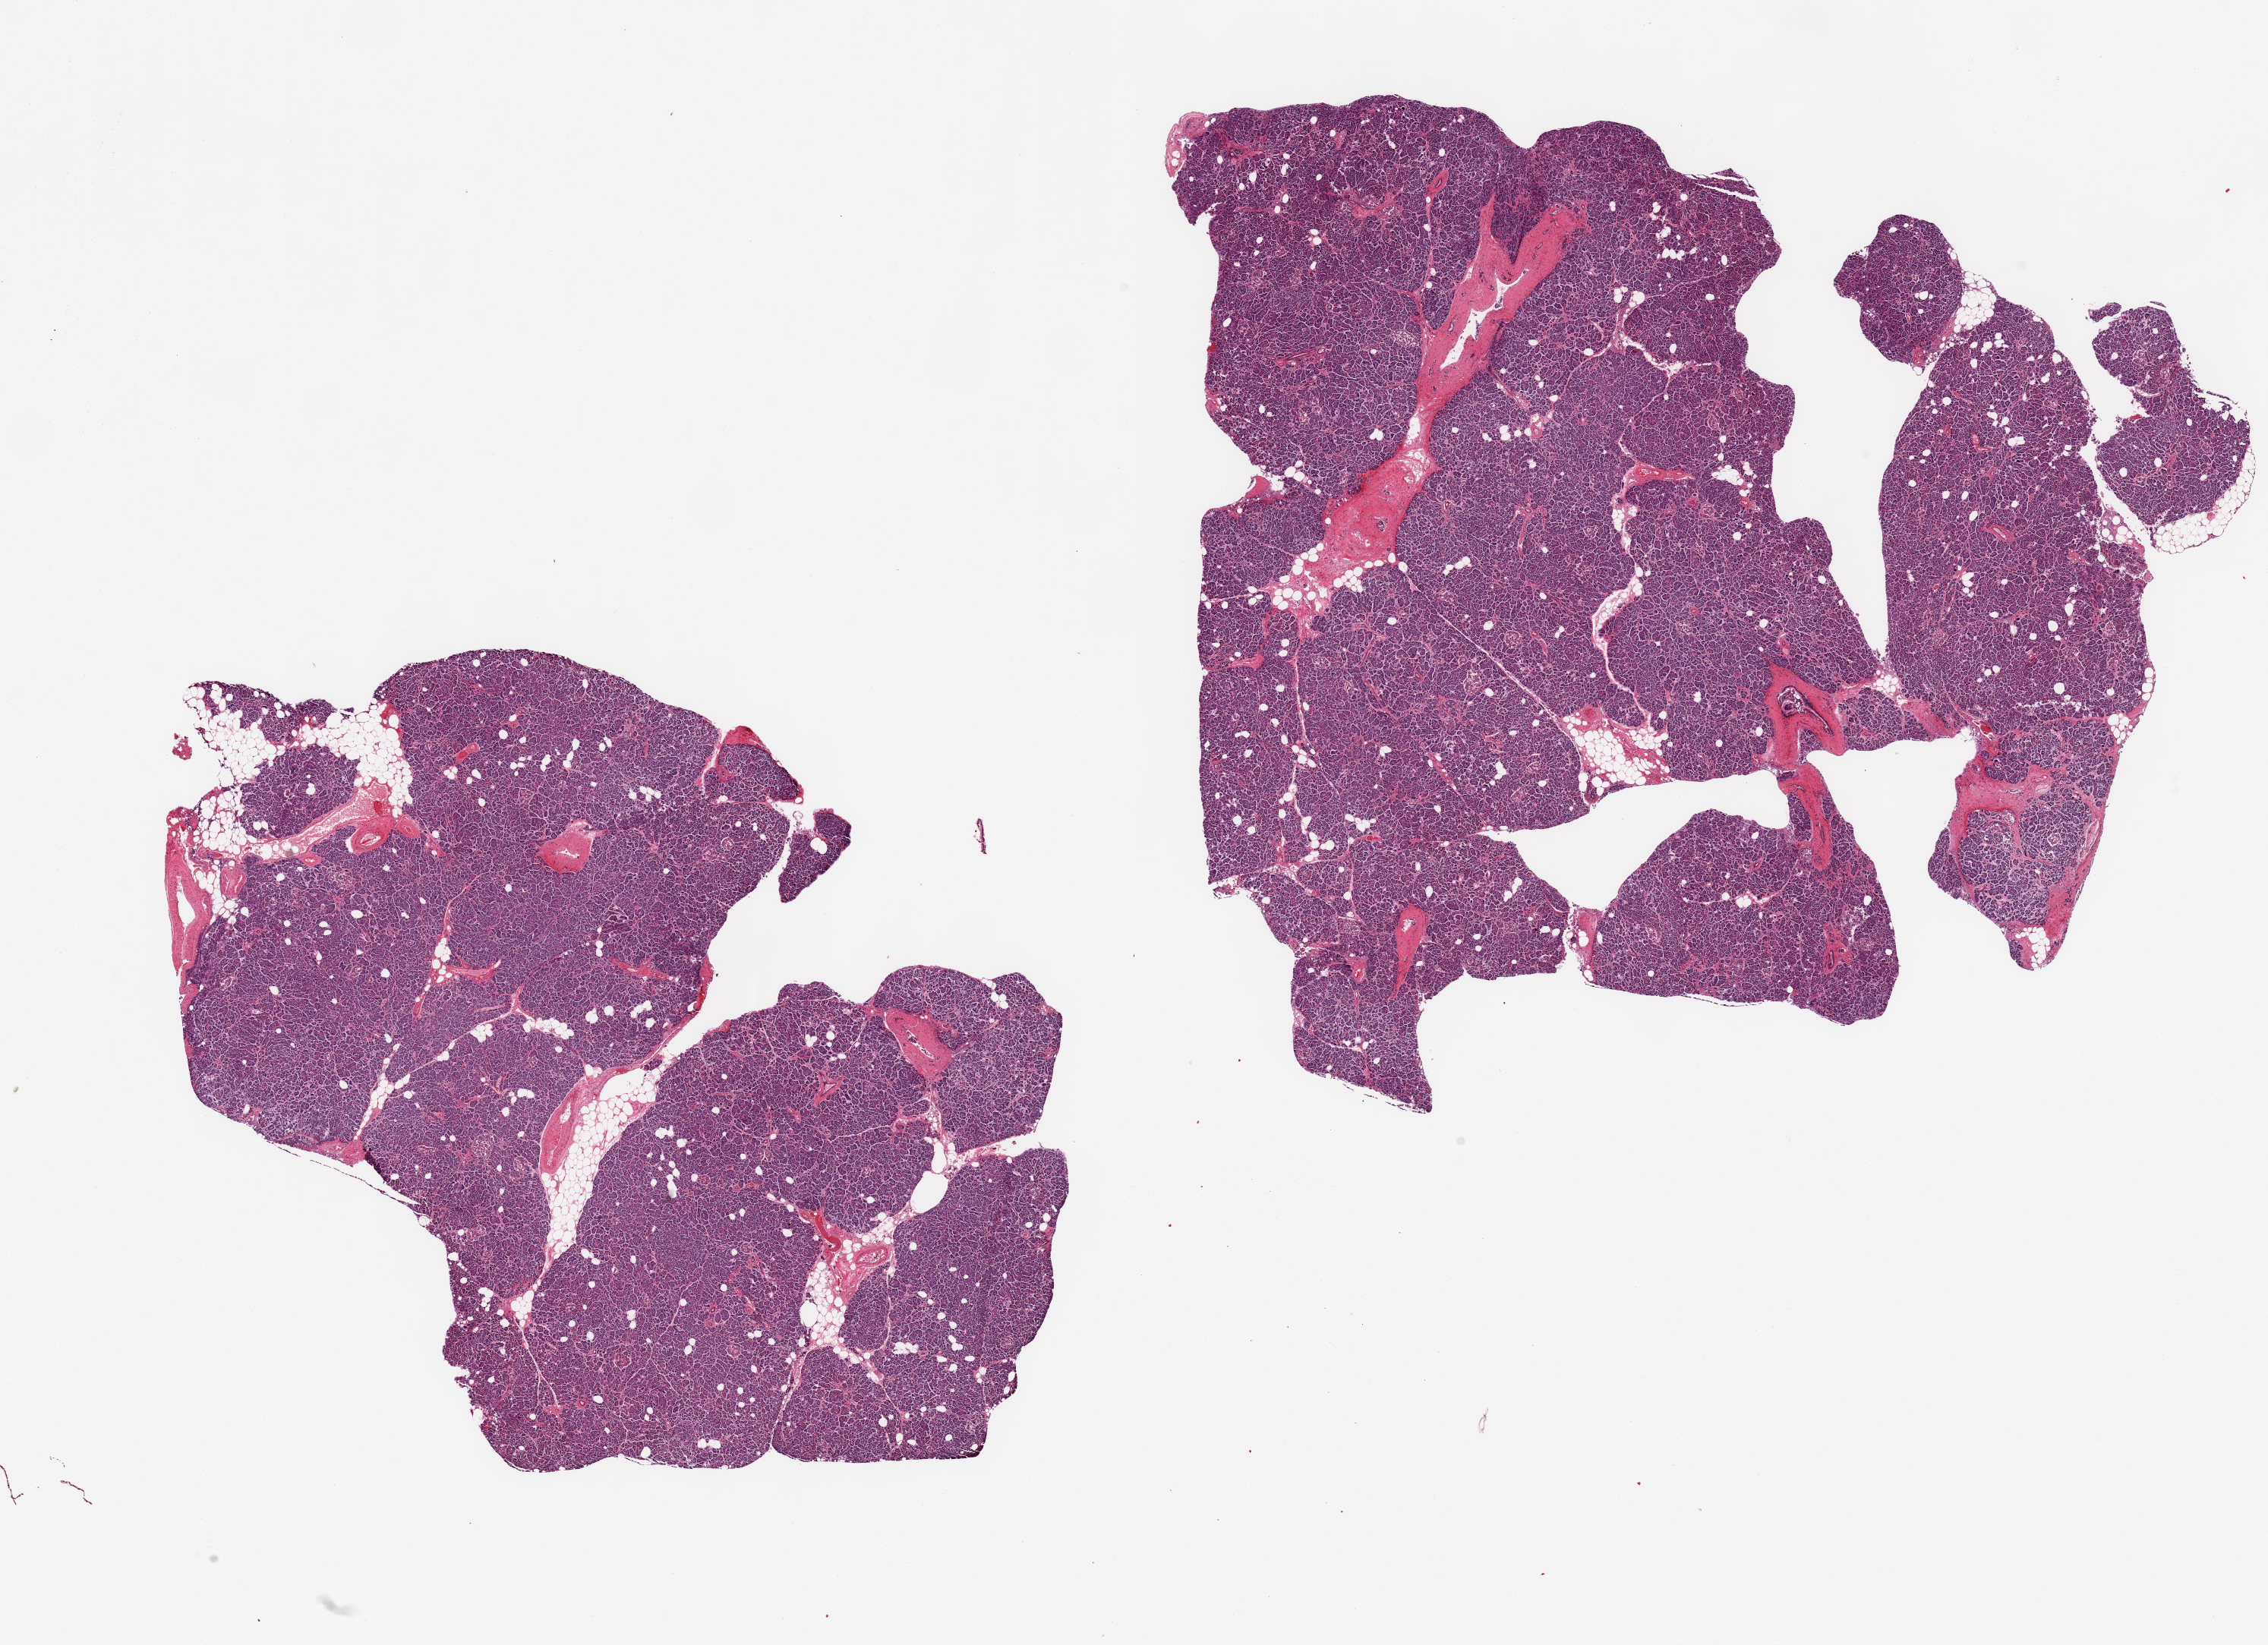
Whole-slide image, H&E stain — whole scanned area (about 23.6 x 17.1 mm, slide scanned at 20x) shown as a low-resolution overview; PAXgene-fixed paraffin-embedded (PFPE) section; section of pancreas (target tissue); donor tissue sample.
Review note (as recorded): 2 pieces autolysis ranges from score '1' to '2' but over all moderately advanced with partially degraded islets.